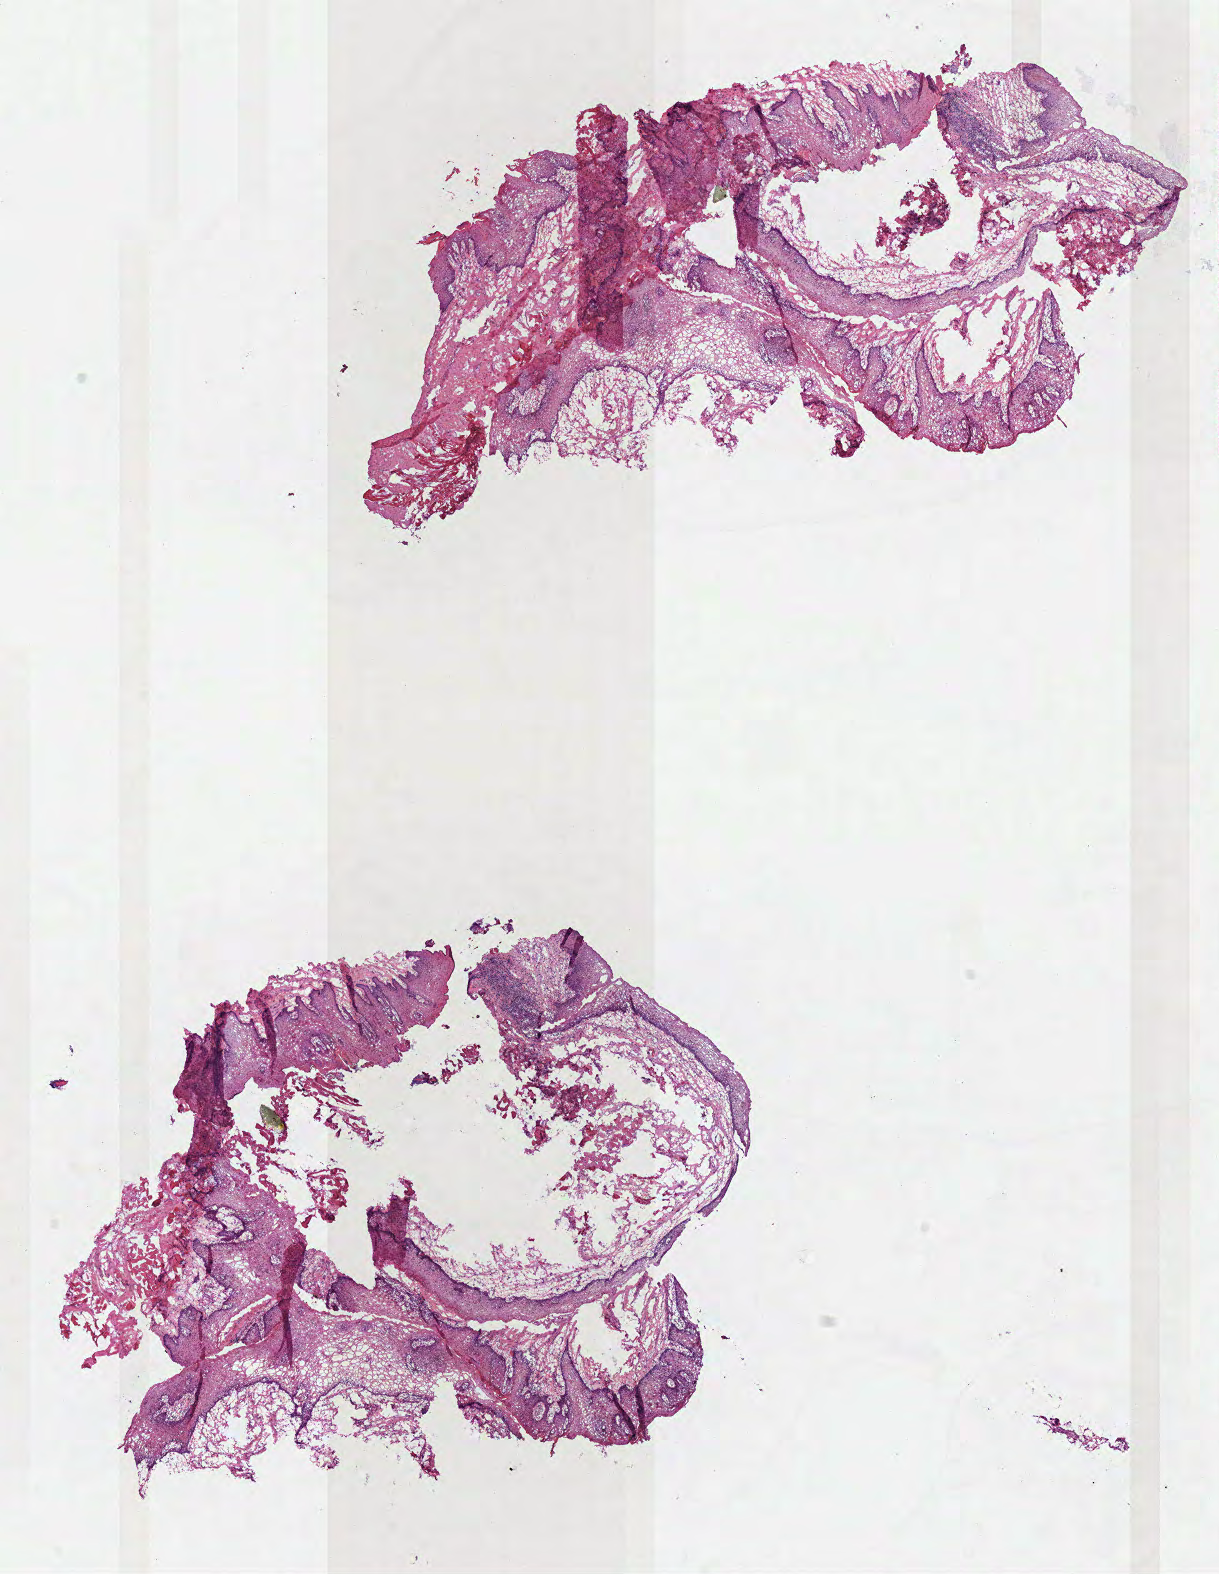
Hematoxylin and eosin (H&E) stained whole-slide image, low-resolution overview of the scanned area, about 9.6 x 12.4 mm (from a 40x scan), frozen section, solid tissue normal (non-tumour tissue) sample from the head and neck. Patient: male, age at initial diagnosis 74 years.
This section: solid tissue normal (non-tumour) sample from the same patient. Patient diagnosis: Squamous cell carcinoma, NOS.